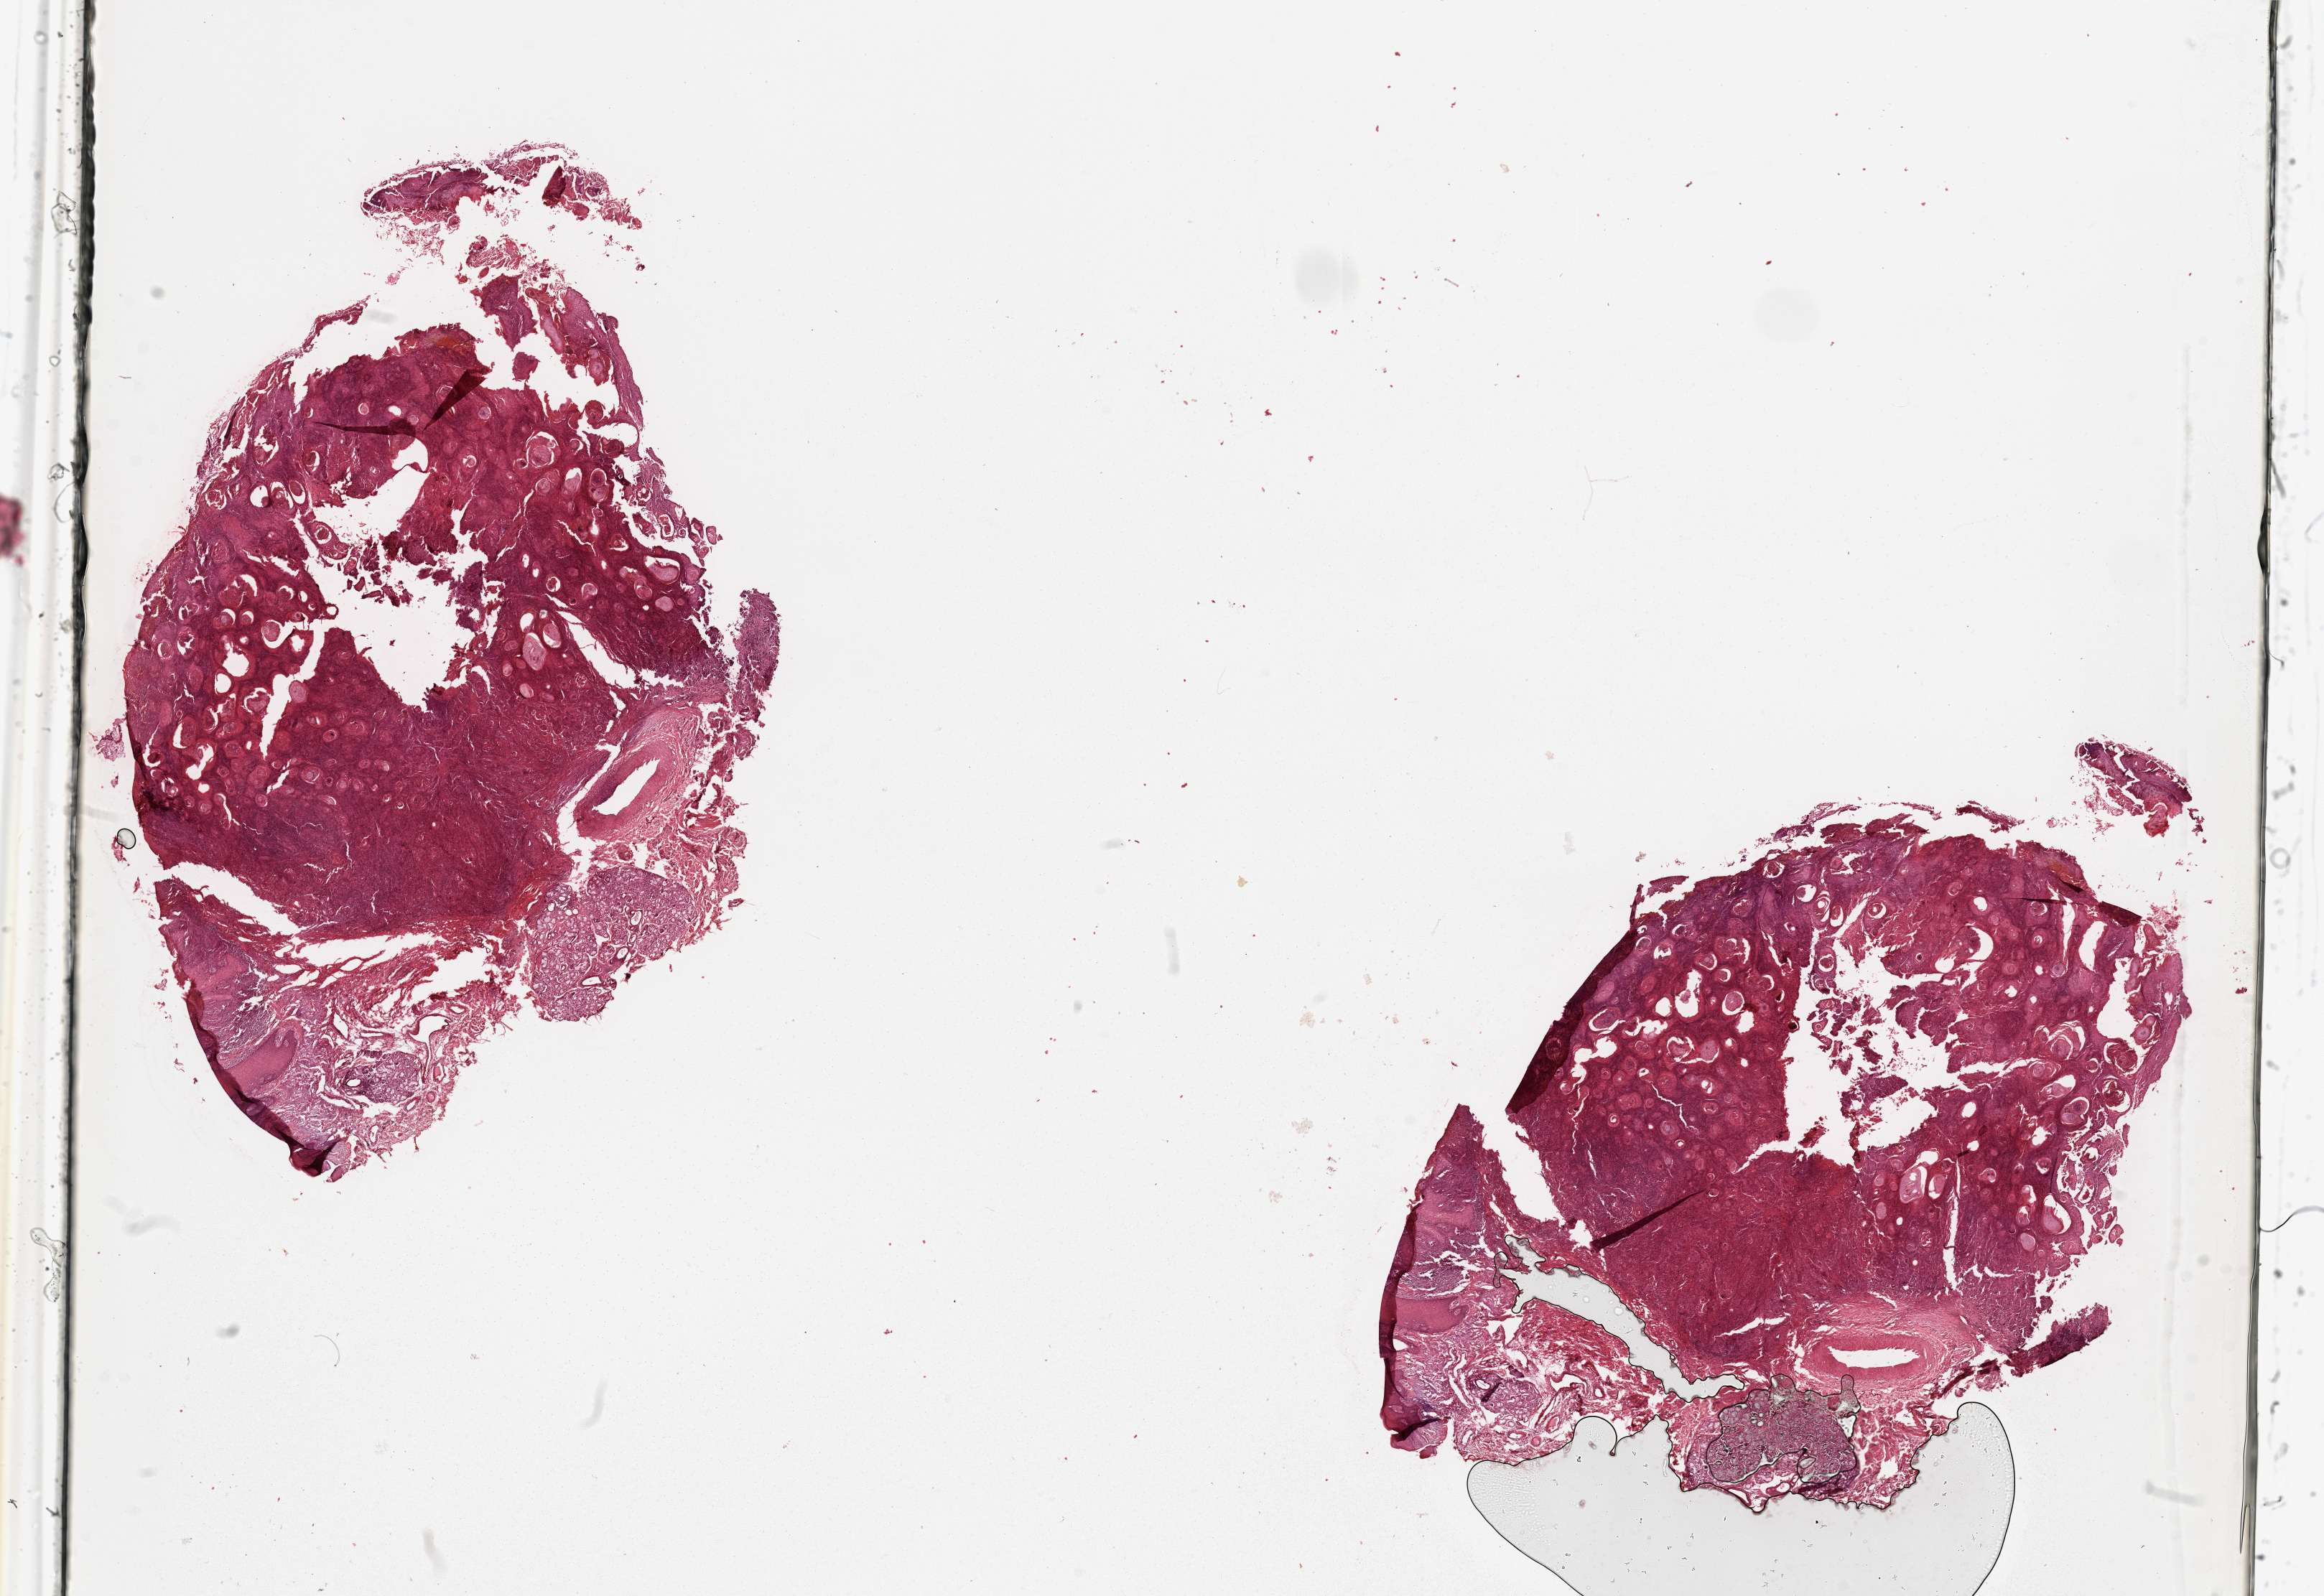
Digitized Hematoxylin and eosin (H&E) stained tissue section (whole slide) — shown as a low-resolution overview of the whole scanned area (about 25.6 x 17.6 mm, from a 20x scan); head and neck, tissue type not recorded. Patient: female, age 80 years.
- patient diagnosis: Squamous cell carcinoma, NOS (lip, NOS)